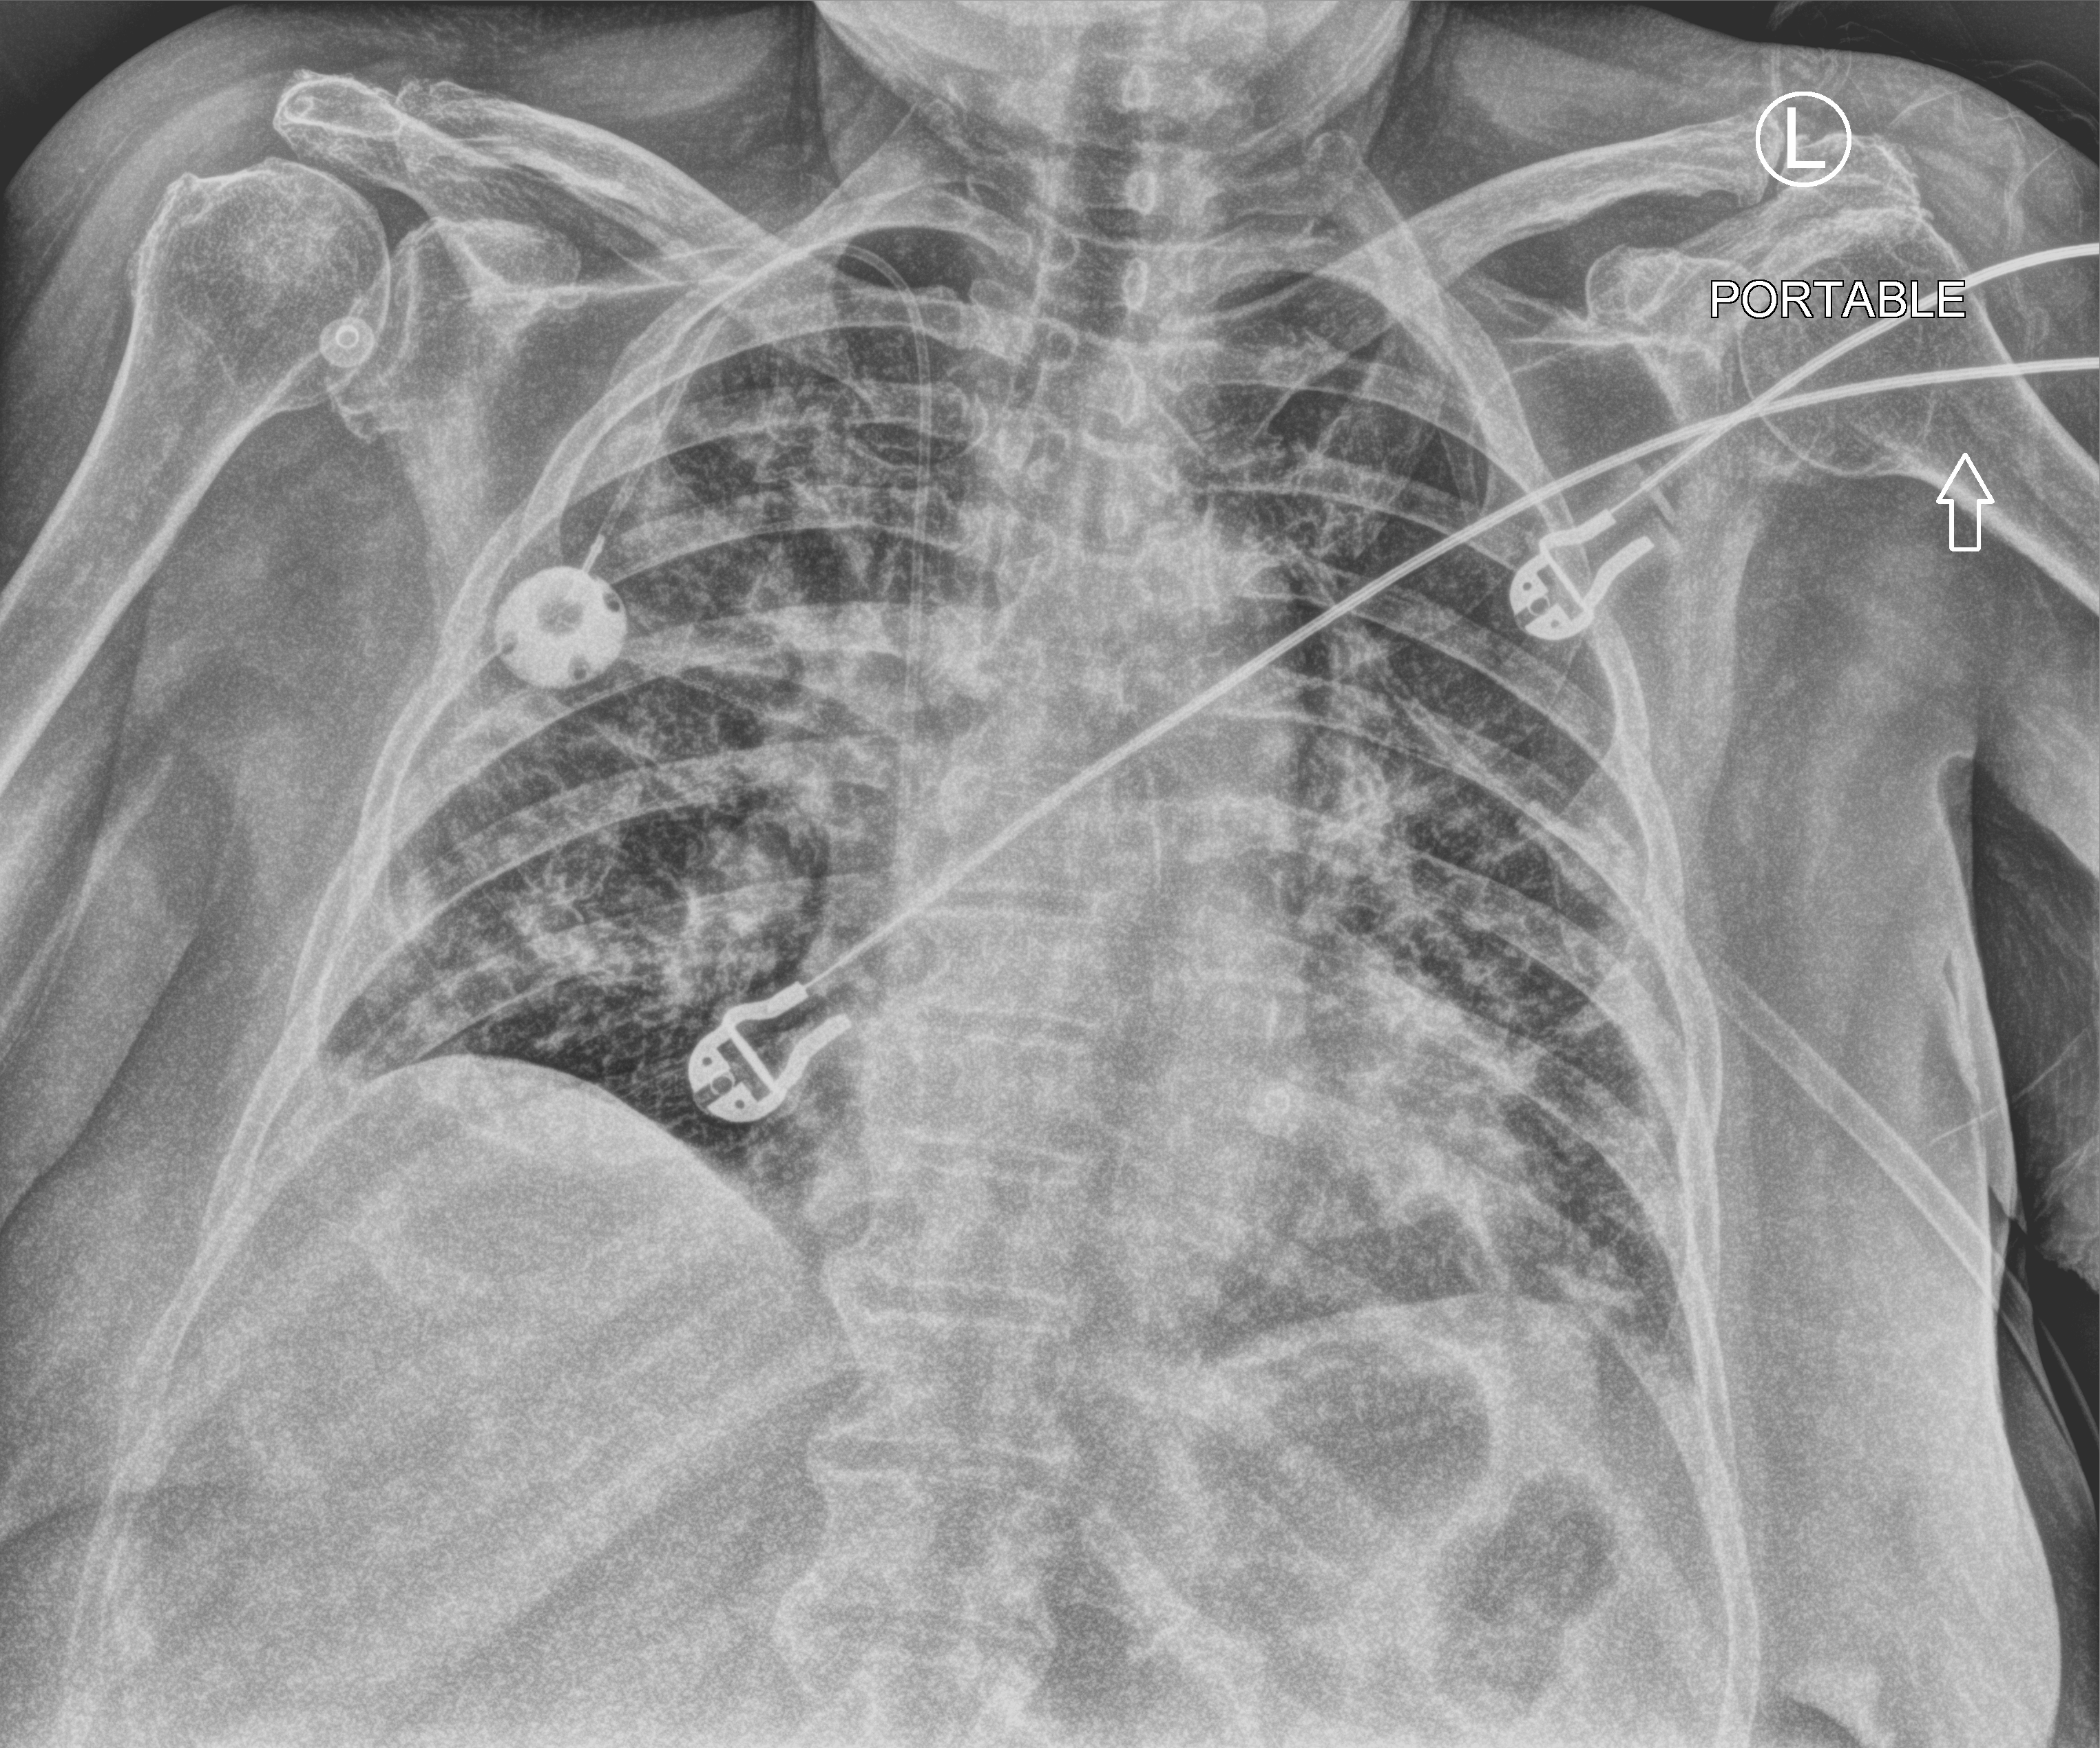
Bedside chest radiograph (computed radiography). Female patient hospitalised with COVID-19, age 75–90 years.
Admission-level facts for this patient (not findings on this image; timing relative to this image not recorded): mechanically ventilated during this hospital stay: no.